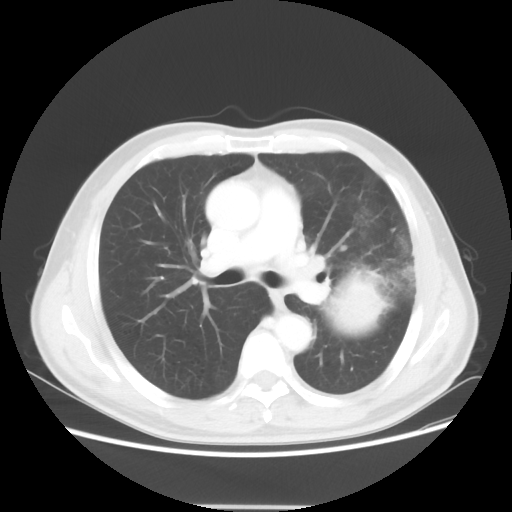
Chest CT, one axial slice; position 32 of 53 along the scan axis; reconstruction kernel STANDARD; 100 kVp; lung window (W 1500 / L -600 HU); 5 mm slice thickness; 512 × 512 image matrix, field of view 391 × 391 mm. Patient: male, 60 years. From the clinical record (not read from this slice): clinical TNM (as recorded): T4 N1 M1a.
Outlined on this slice (rectangle marked by the reading radiologist):
- lung tumour (recorded histology: large cell carcinoma): bounding box [x1, y1, x2, y2] px = [329, 271, 385, 330]